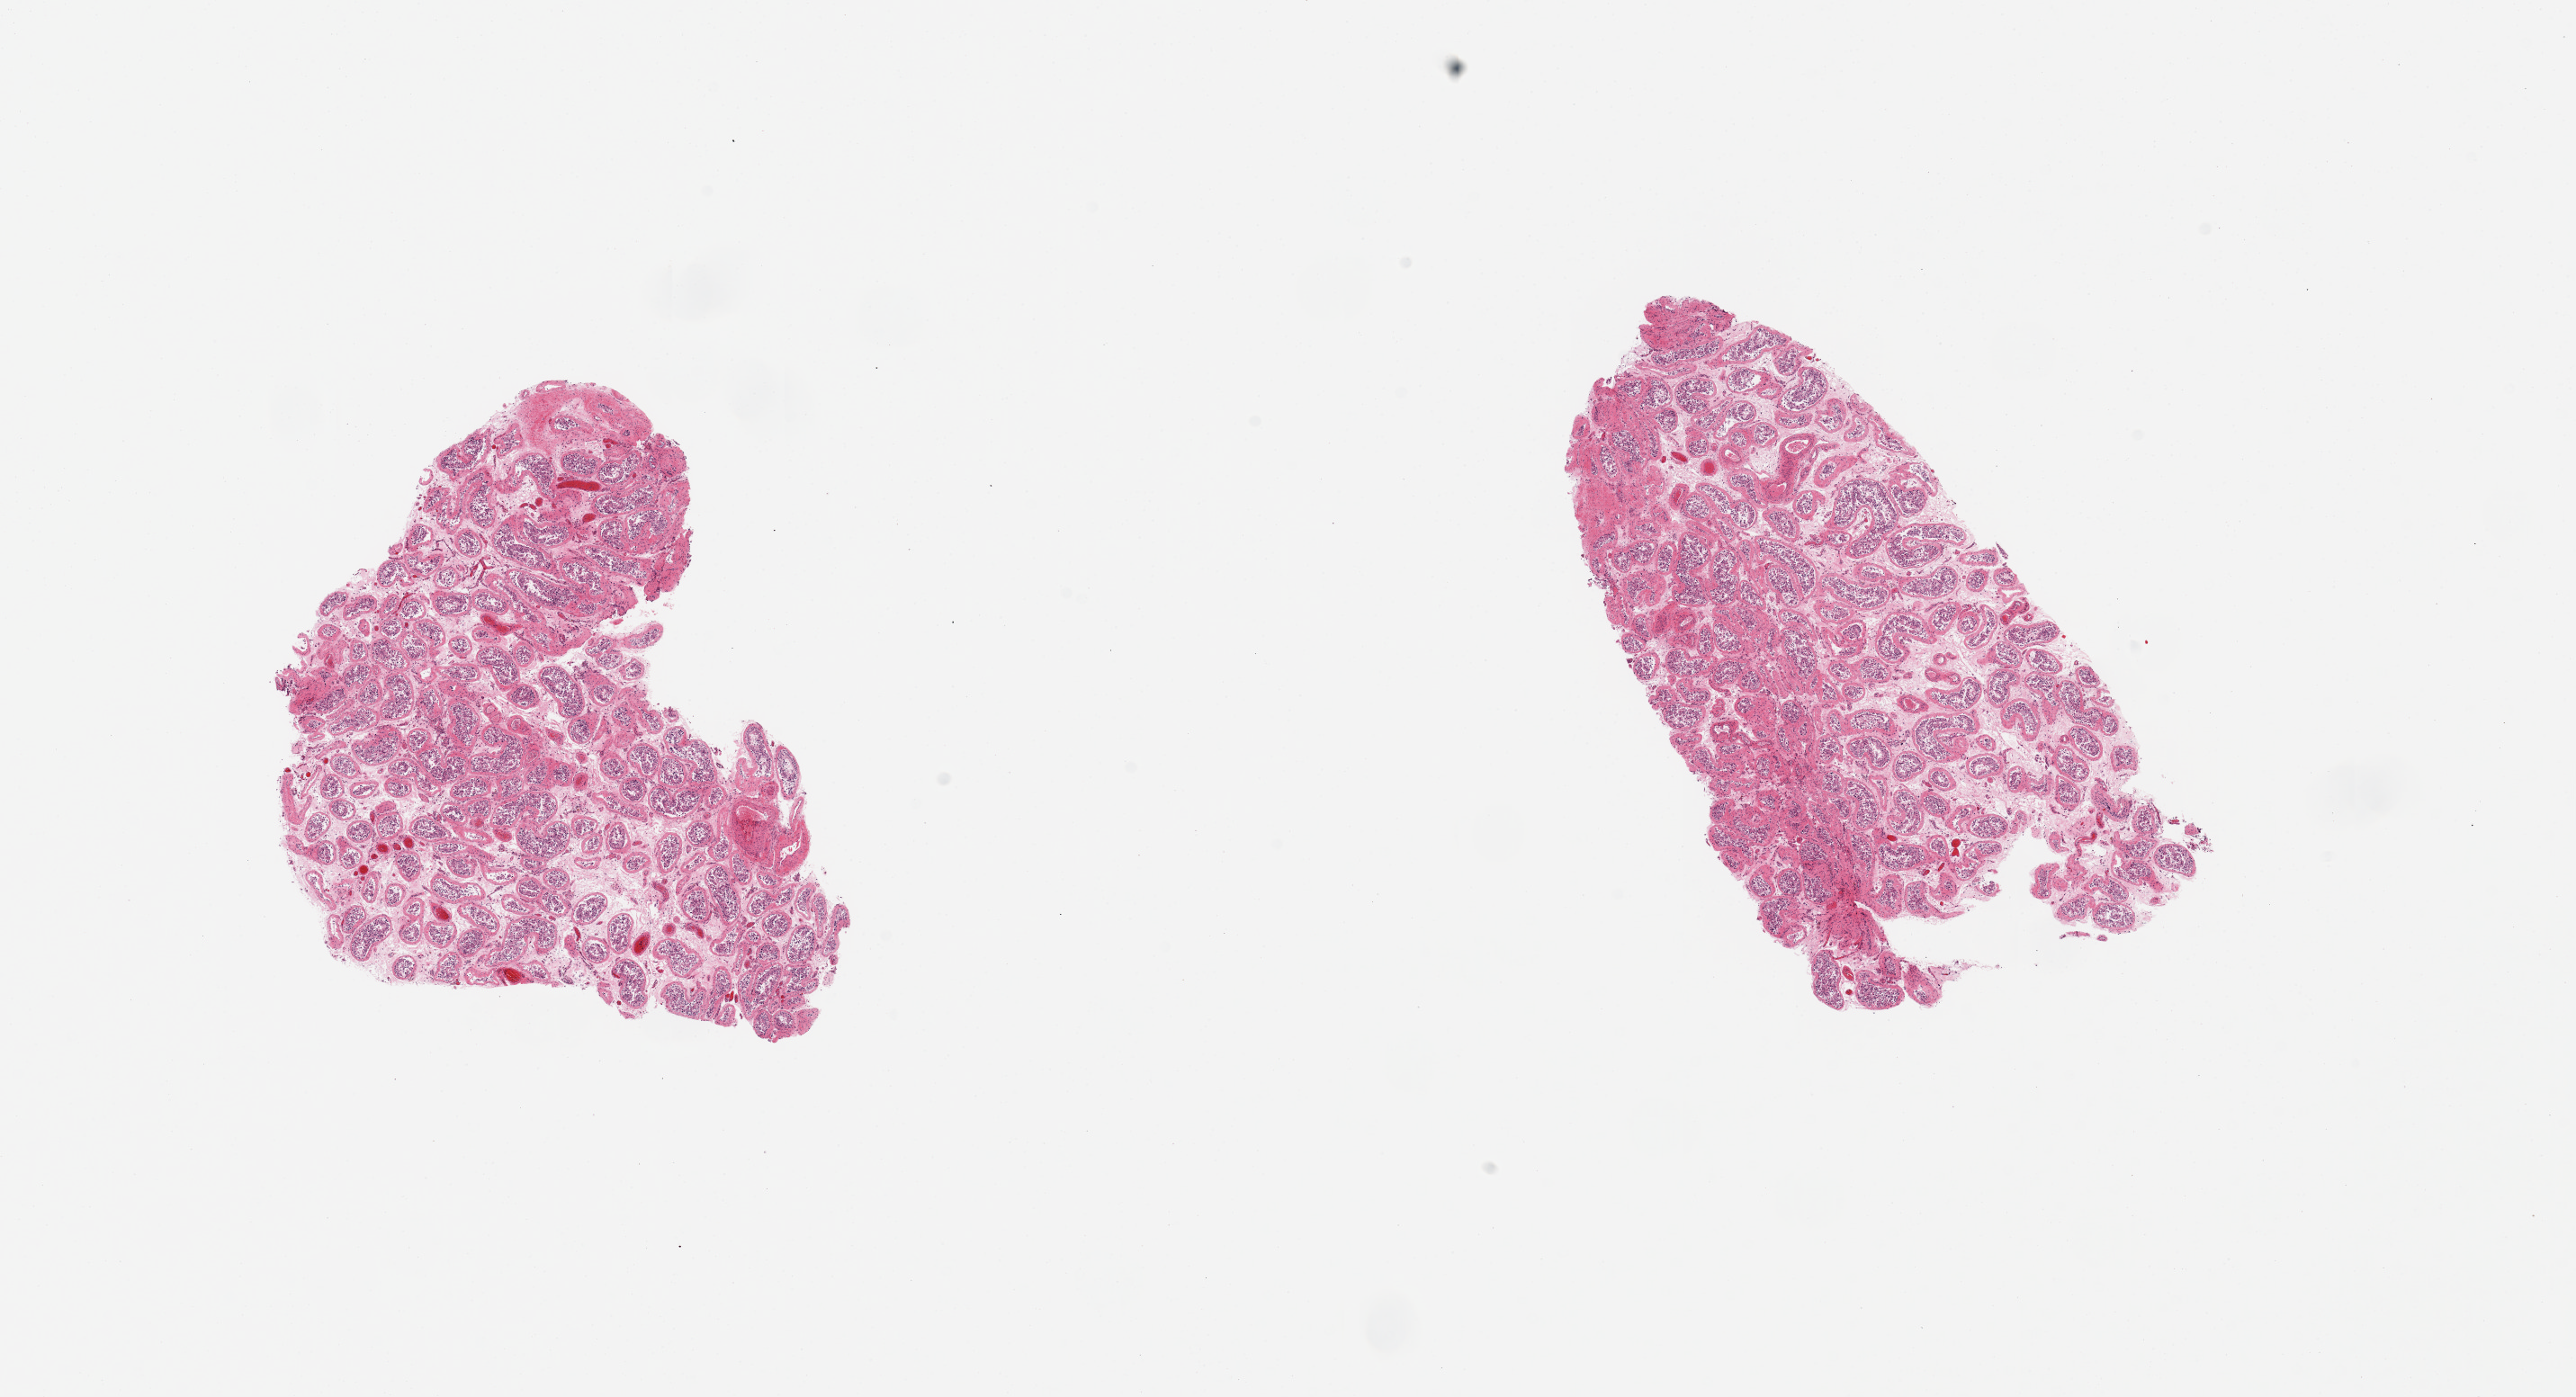
Whole-slide image, haematoxylin and eosin stain, brightfield, whole scanned area (about 22.6 x 12.3 mm) shown as a low-resolution overview. PAXgene-fixed paraffin-embedded (PFPE) section. Sampled site (target tissue): testis. Donor tissue sample. Donor sex: male.
* reviewer comment on this tissue sample: 2 pieces tubules with severa autolysis, apparent reduced spermatogenesis